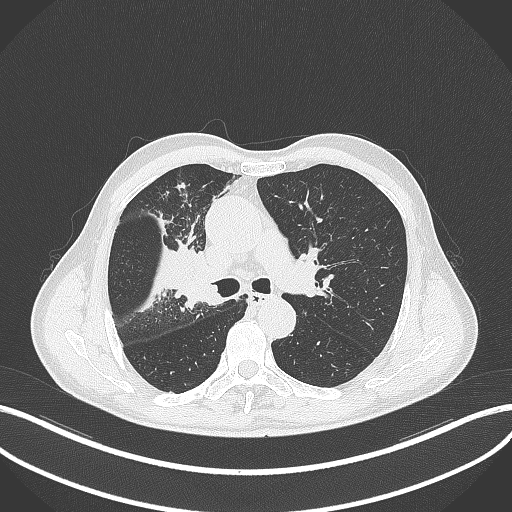
Chest CT, one axial slice; slice 312 of 490 in the series (ordered by position); reconstruction kernel B70f; lung window (W 1500 / L -600 HU); 1 mm slice thickness; 512 × 512 image matrix, field of view 400 × 400 mm. Patient: male, 69 years. From the clinical record (not read from this slice): clinical TNM (as recorded): T2a N0 M0.
Annotated regions visible in this slice (rectangle marked by the reading radiologist):
- lung tumour (recorded histology: adenocarcinoma): bounding box <168,240,222,314> (left, top, right, bottom; pixels)